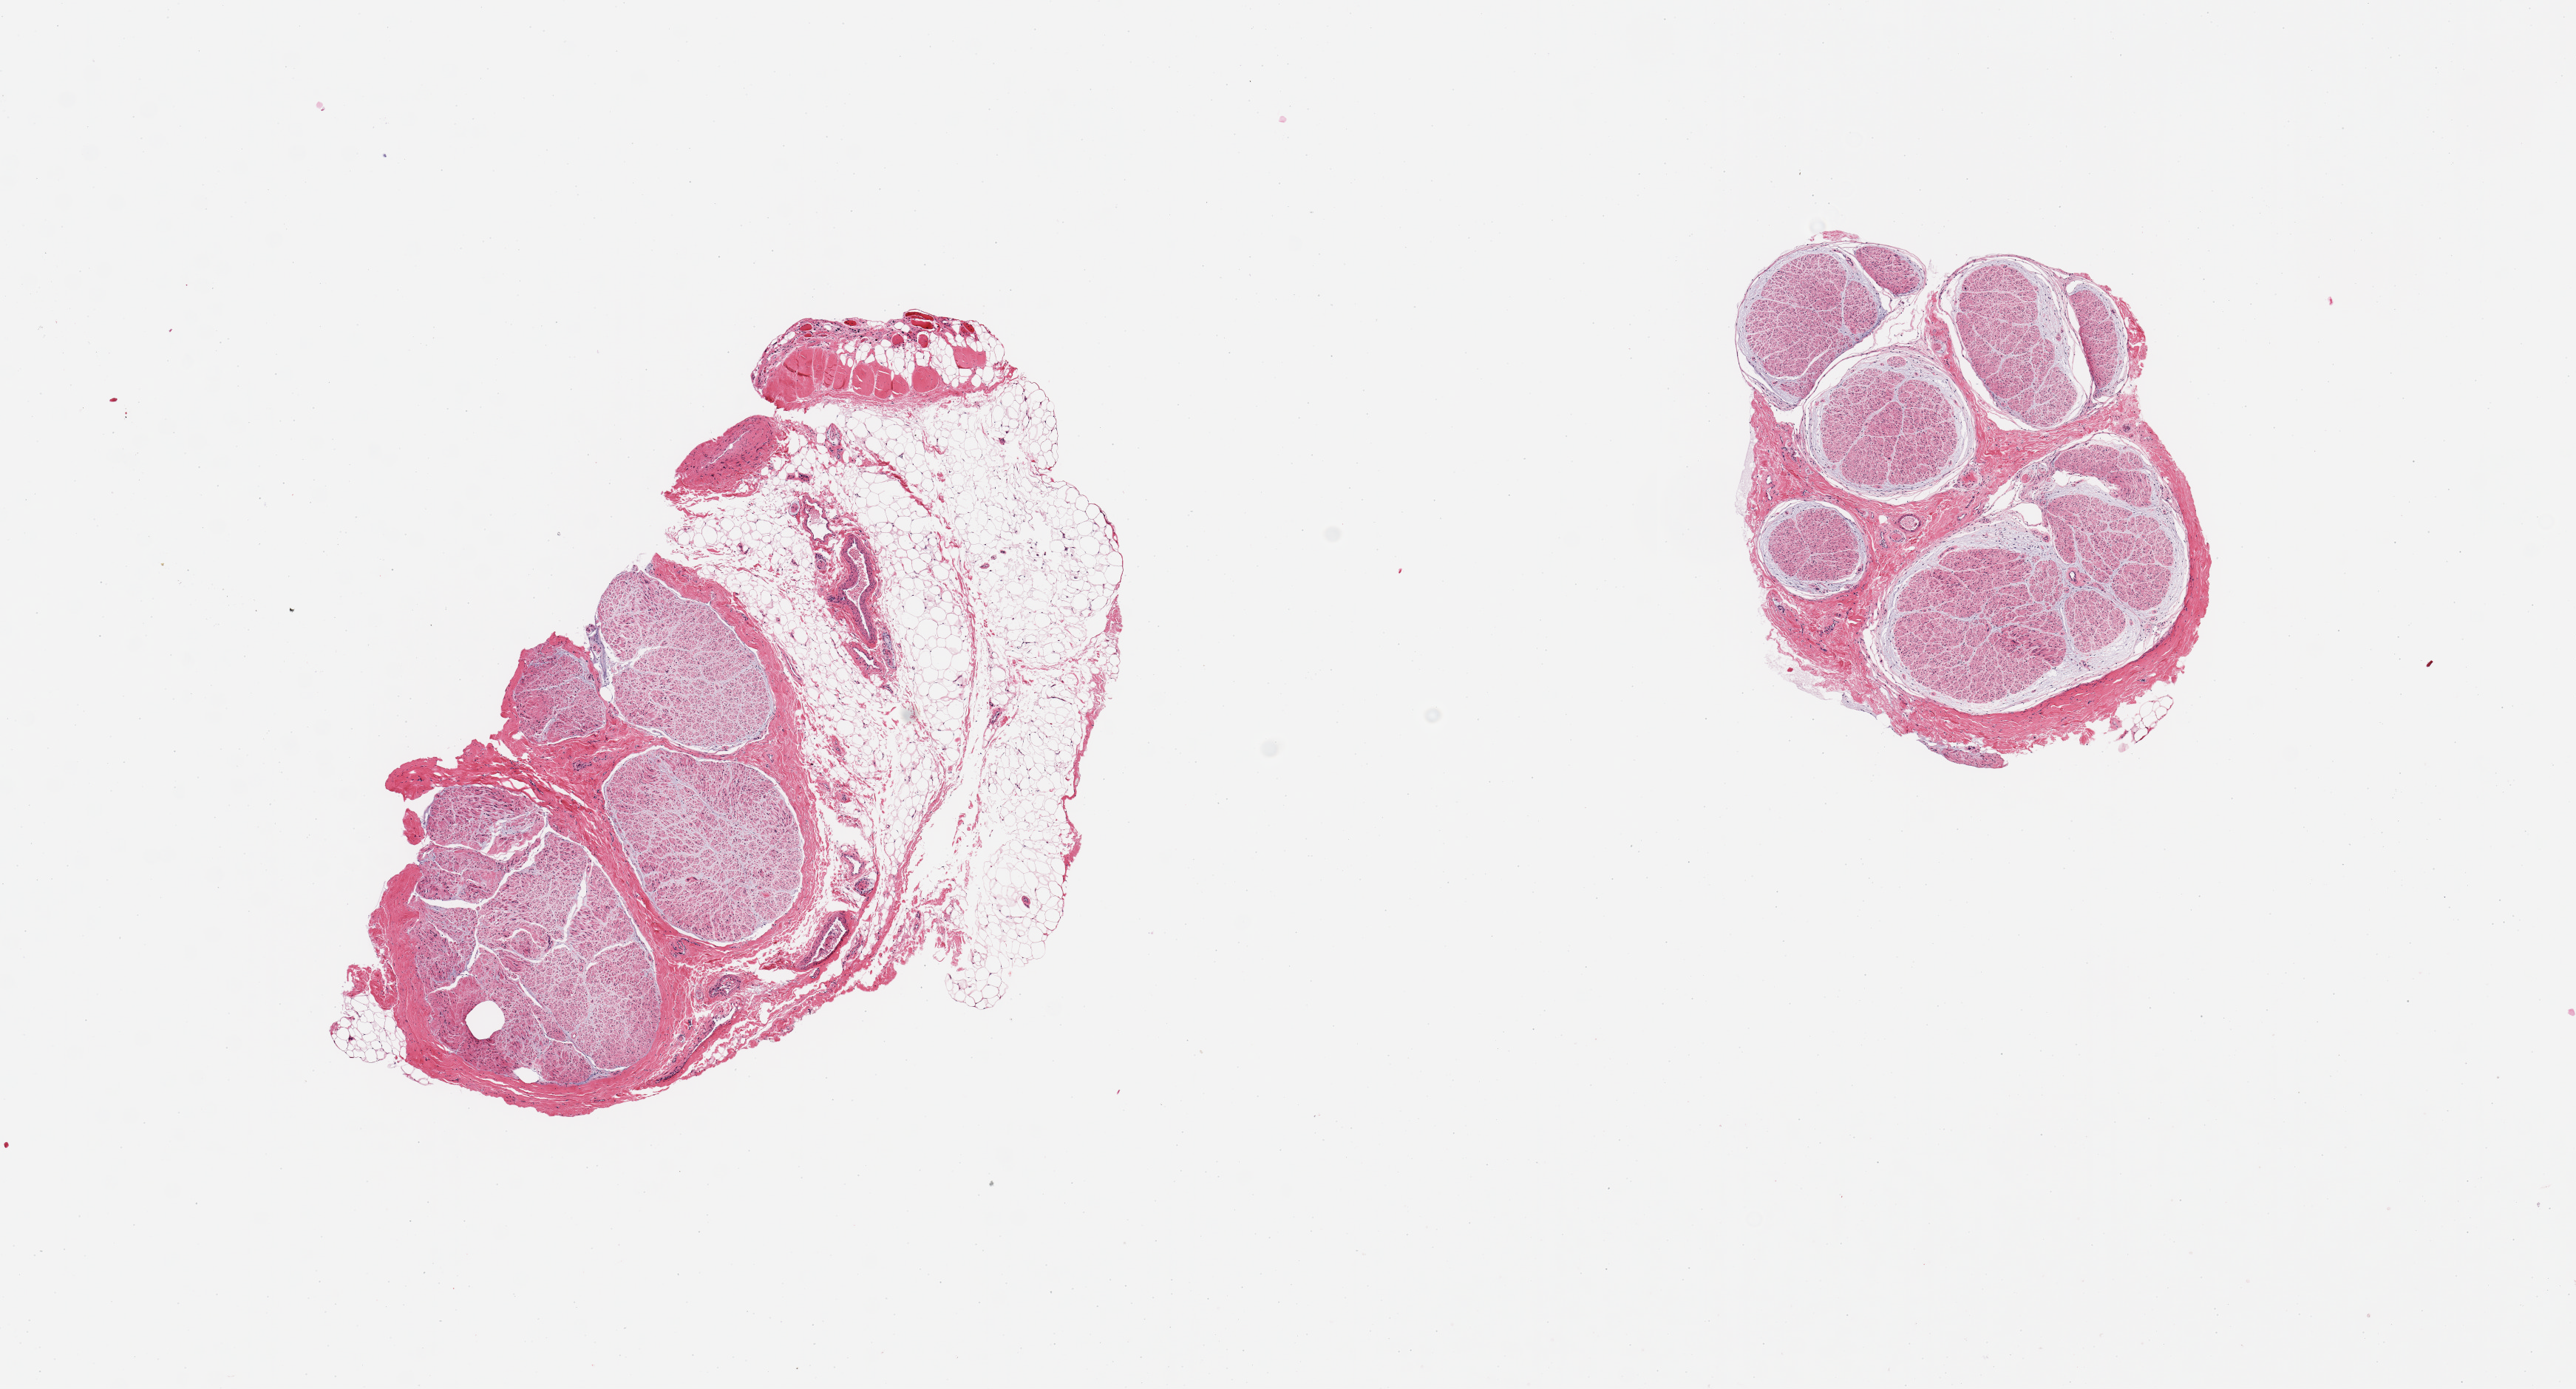
Digitized haematoxylin and eosin-stained section, a low-resolution overview of the entire scanned area, about 13.8 x 7.4 mm (acquisition: 20x scan); PAXgene-fixed, paraffin-embedded tissue; sampled site (target tissue): tibial nerve; tissue donor sample. Female donor.
Review note (as recorded): 2 pieces; one piece is ~50% fat/tendon.